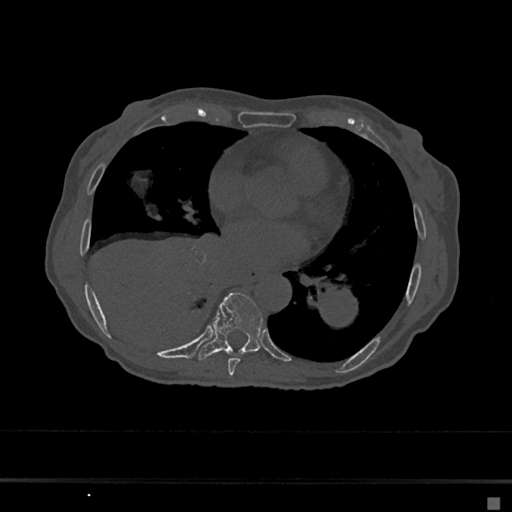
CT including the spine, one axial slice; slice 341 of 797 in the series (ordered by position); bone window (W 1800 / L 400 HU); 0.5 mm slice thickness; 512 × 512 image matrix, field of view 360 × 360 mm. Patient: female, 68 years. Case-level facts recorded for this patient, not image findings: primary cancer: renal.
Annotated regions visible in this slice (semi-automatically segmented with operator editing):
- T7 vertebra: box from (x=228, y=358) to (x=240, y=376) px
- T8 vertebra: (x=198, y=292)–(x=263, y=361)